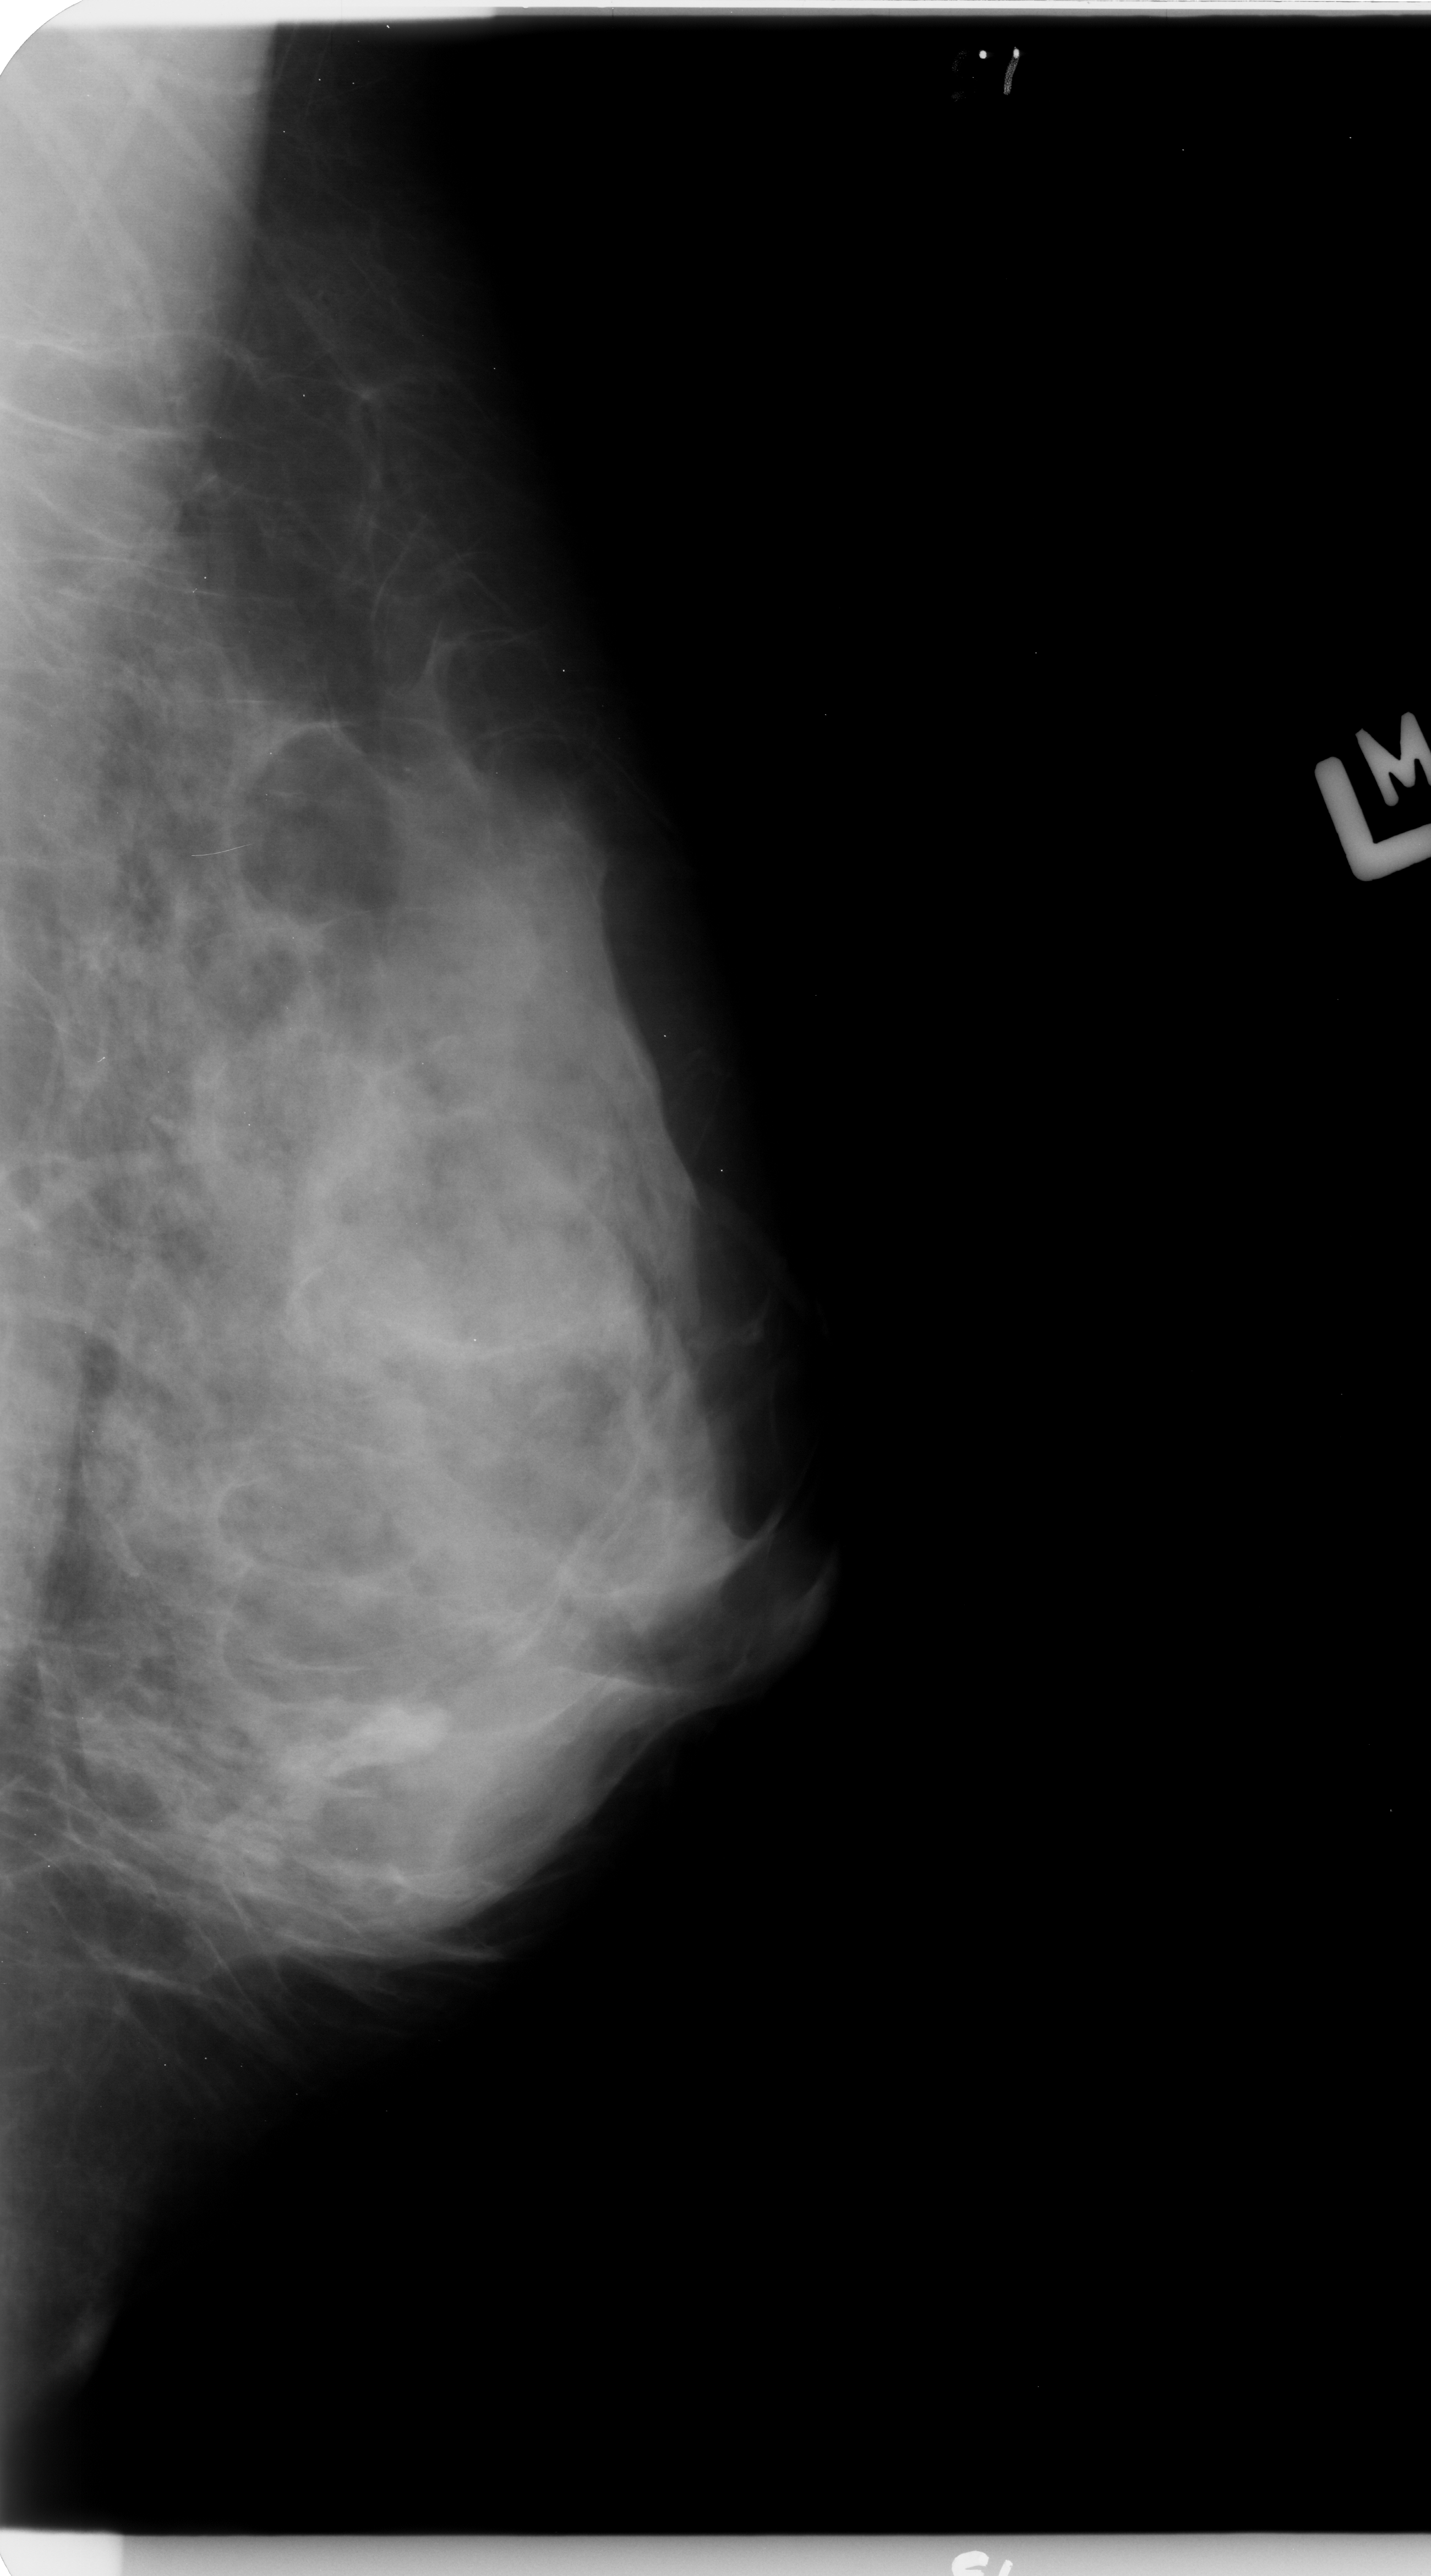
Mammogram (digitized film), left breast, MLO view, BI-RADS breast density category 4 (scale 1–4).
Abnormality record for this image: mass, shape irregular, margins circumscribed / obscured; BI-RADS assessment category 4; pathology (as recorded): benign.